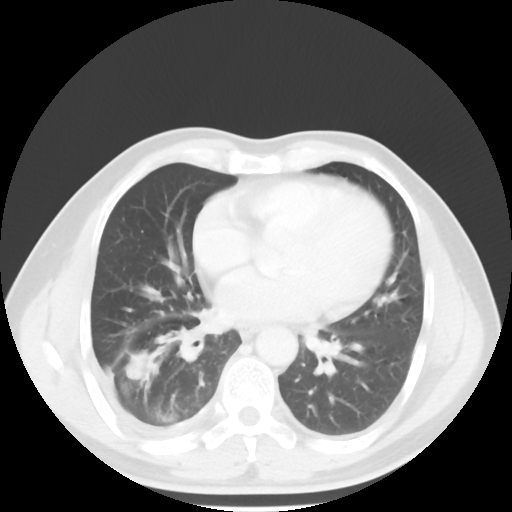
Chest CT, one axial slice. Position 24 of 56 along the scan axis. 120 kVp. Lung window (W 1500 / L -600 HU). 5 mm slice thickness. 512 × 512 image matrix, field of view 344 × 344 mm. Patient: male, 56 years. Case-level facts recorded for this patient, not image findings: clinical TNM (as recorded): T2 N3 M1.
Structures marked on this image (rectangle marked by the reading radiologist):
- lung tumour (recorded histology: adenocarcinoma): bounding box (x1, y1, x2, y2) in pixels: (124, 341, 159, 383)